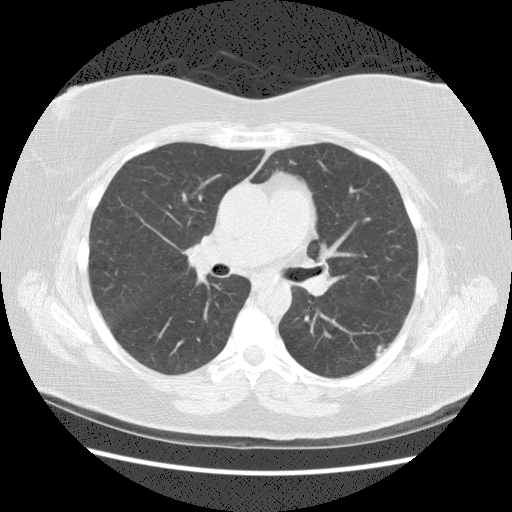
Chest CT (low-dose screening protocol), one axial image. Second screening round (one year after baseline). Lung window (W 1500 / L -600 HU). 2.5 mm slice thickness. Slice 81 of 140 in the series. Female participant, aged 57 years at enrolment. Current smoker at enrolment.
- Lesion marked by an expert reader, bounding box [x1, y1, x2, y2] px = [359, 328, 402, 369].
- The exam's reader record, not a measurement of the box and not confirmed to be the same lesion: non-calcified nodule or mass ≥4 mm, left lower lobe, 19 × 9 mm, poorly defined margins, mixed attenuation, pre-existing on the prior screen: yes; interval growth: yes.
- Official screen result: positive, other.
- Lung cancer was diagnosed 560 days after this screen (after the third annual screen): squamous cell carcinoma, NOS, left lower lobe, poorly differentiated (G3), stage IB (AJCC 6th edition), 40 mm at pathology.